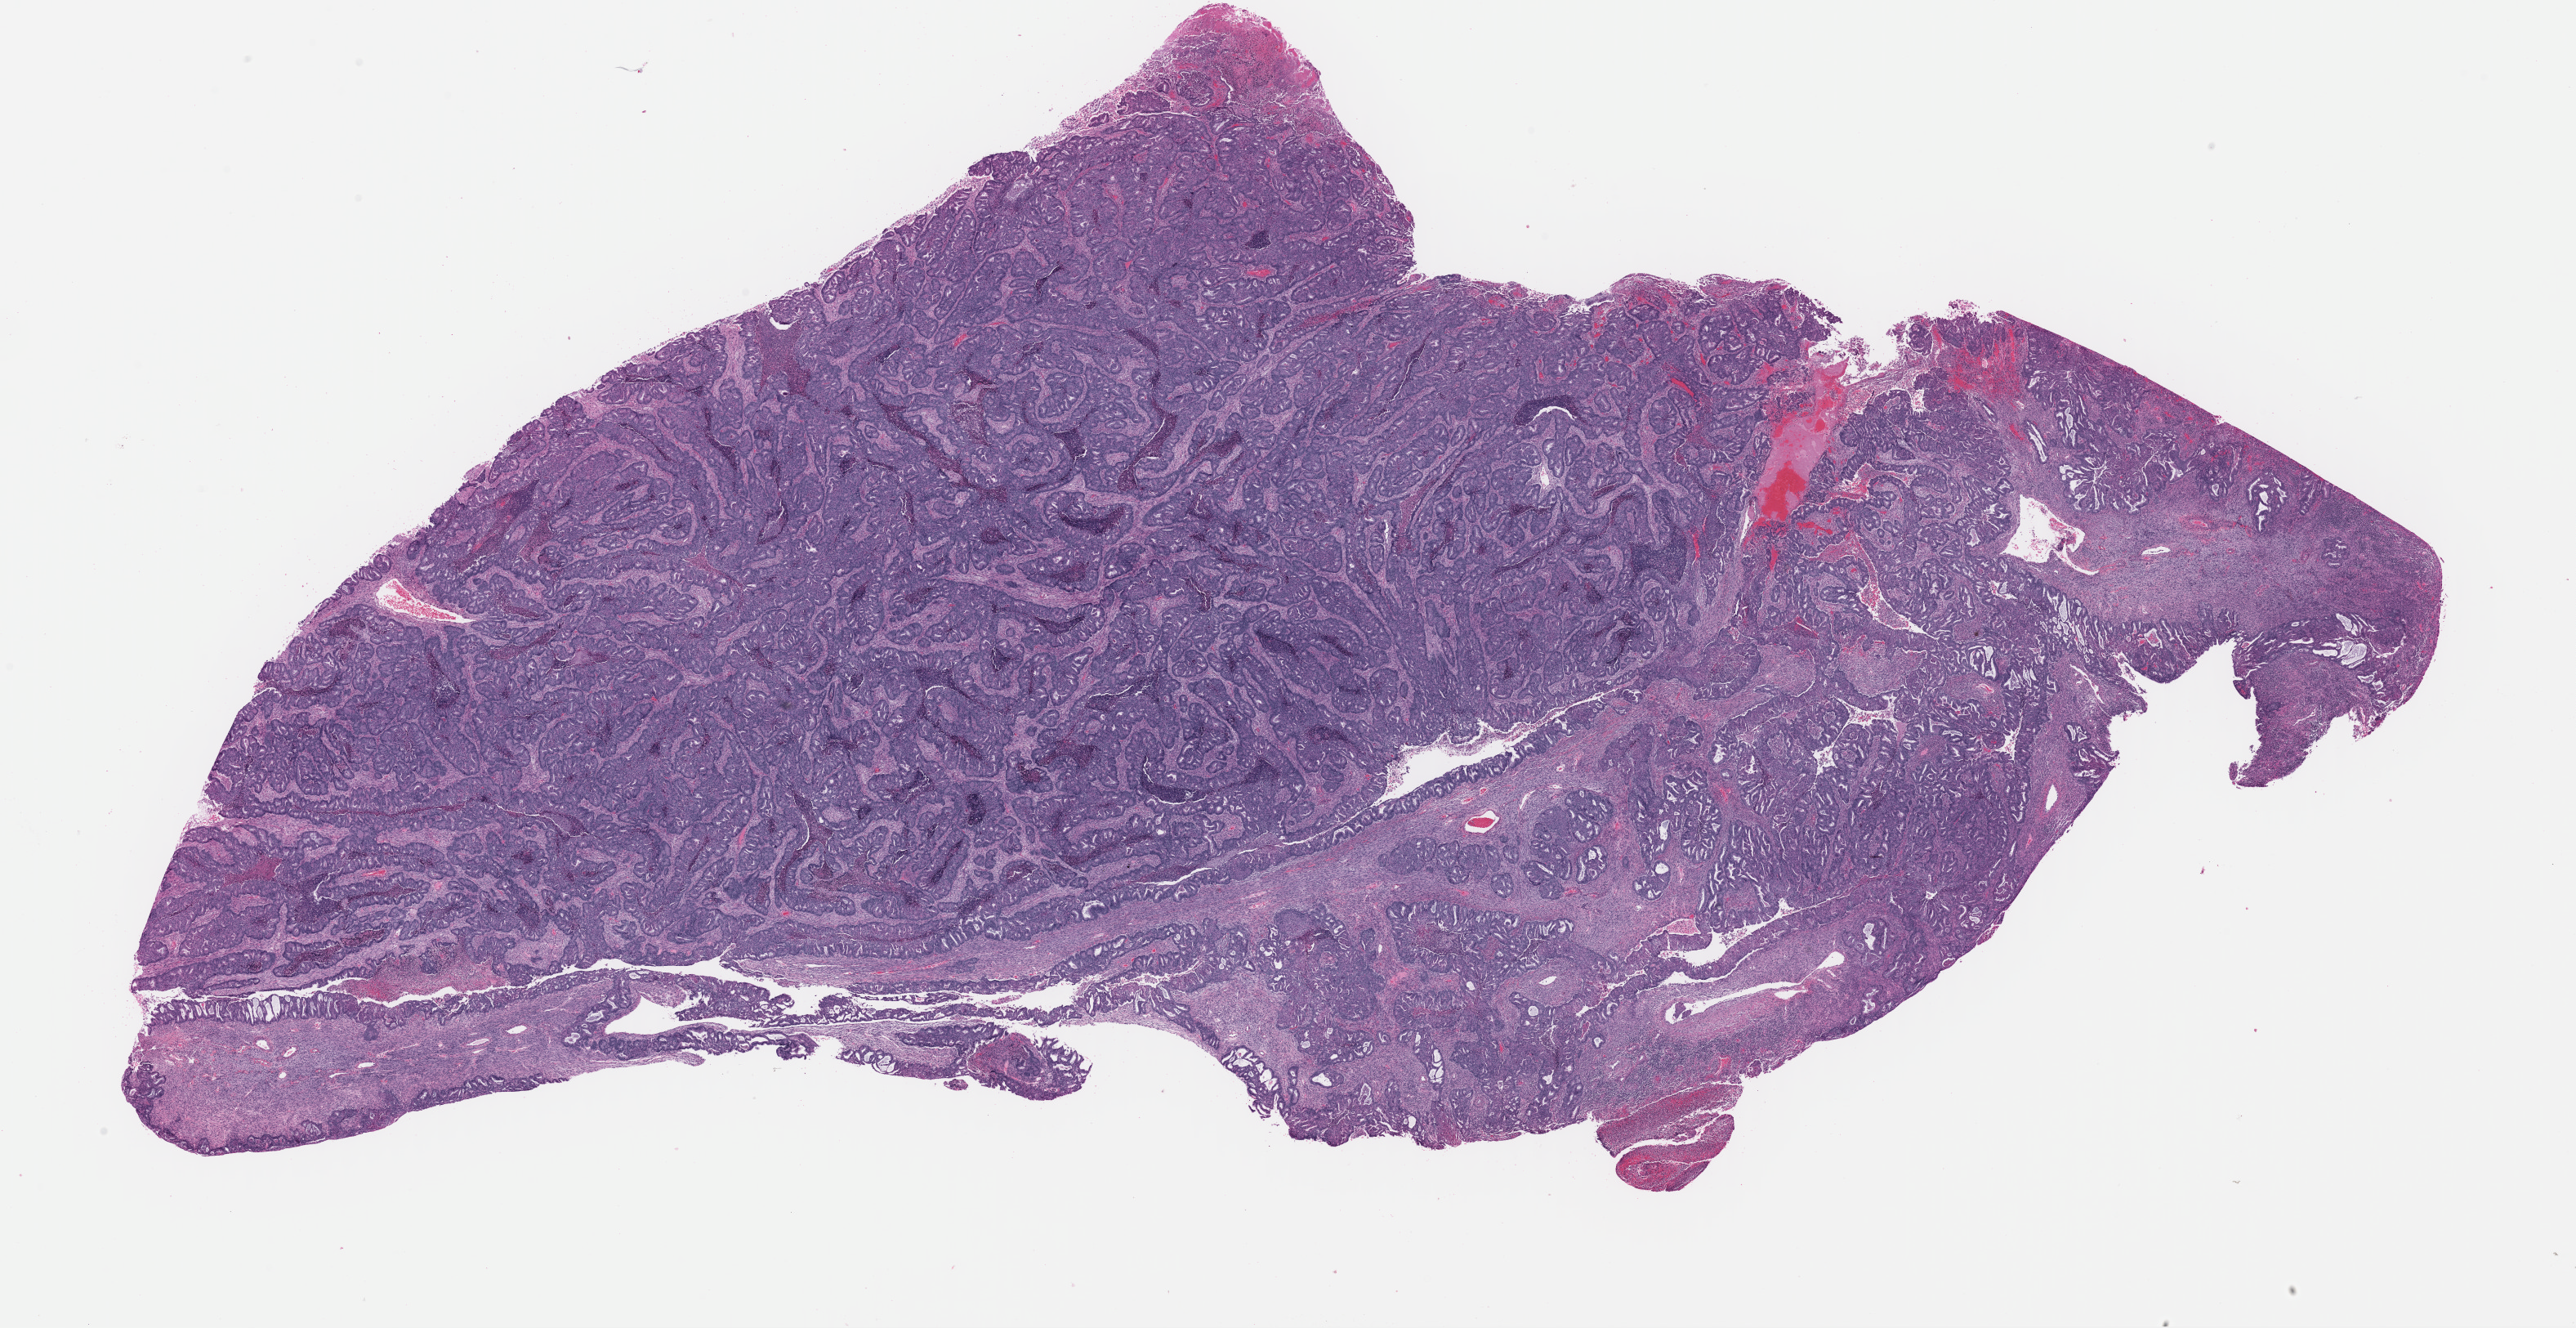
Digitized H&E tissue section (whole slide) — a low-resolution overview of the entire scanned area, about 24.9 x 12.8 mm (from a 40x scan). Formalin-fixed paraffin-embedded (FFPE) diagnostic section. Uterus, primary tumour sample. Patient: female, age at initial diagnosis 51 years. Histologic grade: G2 (moderately differentiated).
• diagnosis: Endometrioid adenocarcinoma, NOS (endometrium)
• lymph nodes positive (case pathology): 0 of 6 examined
• FIGO stage: II